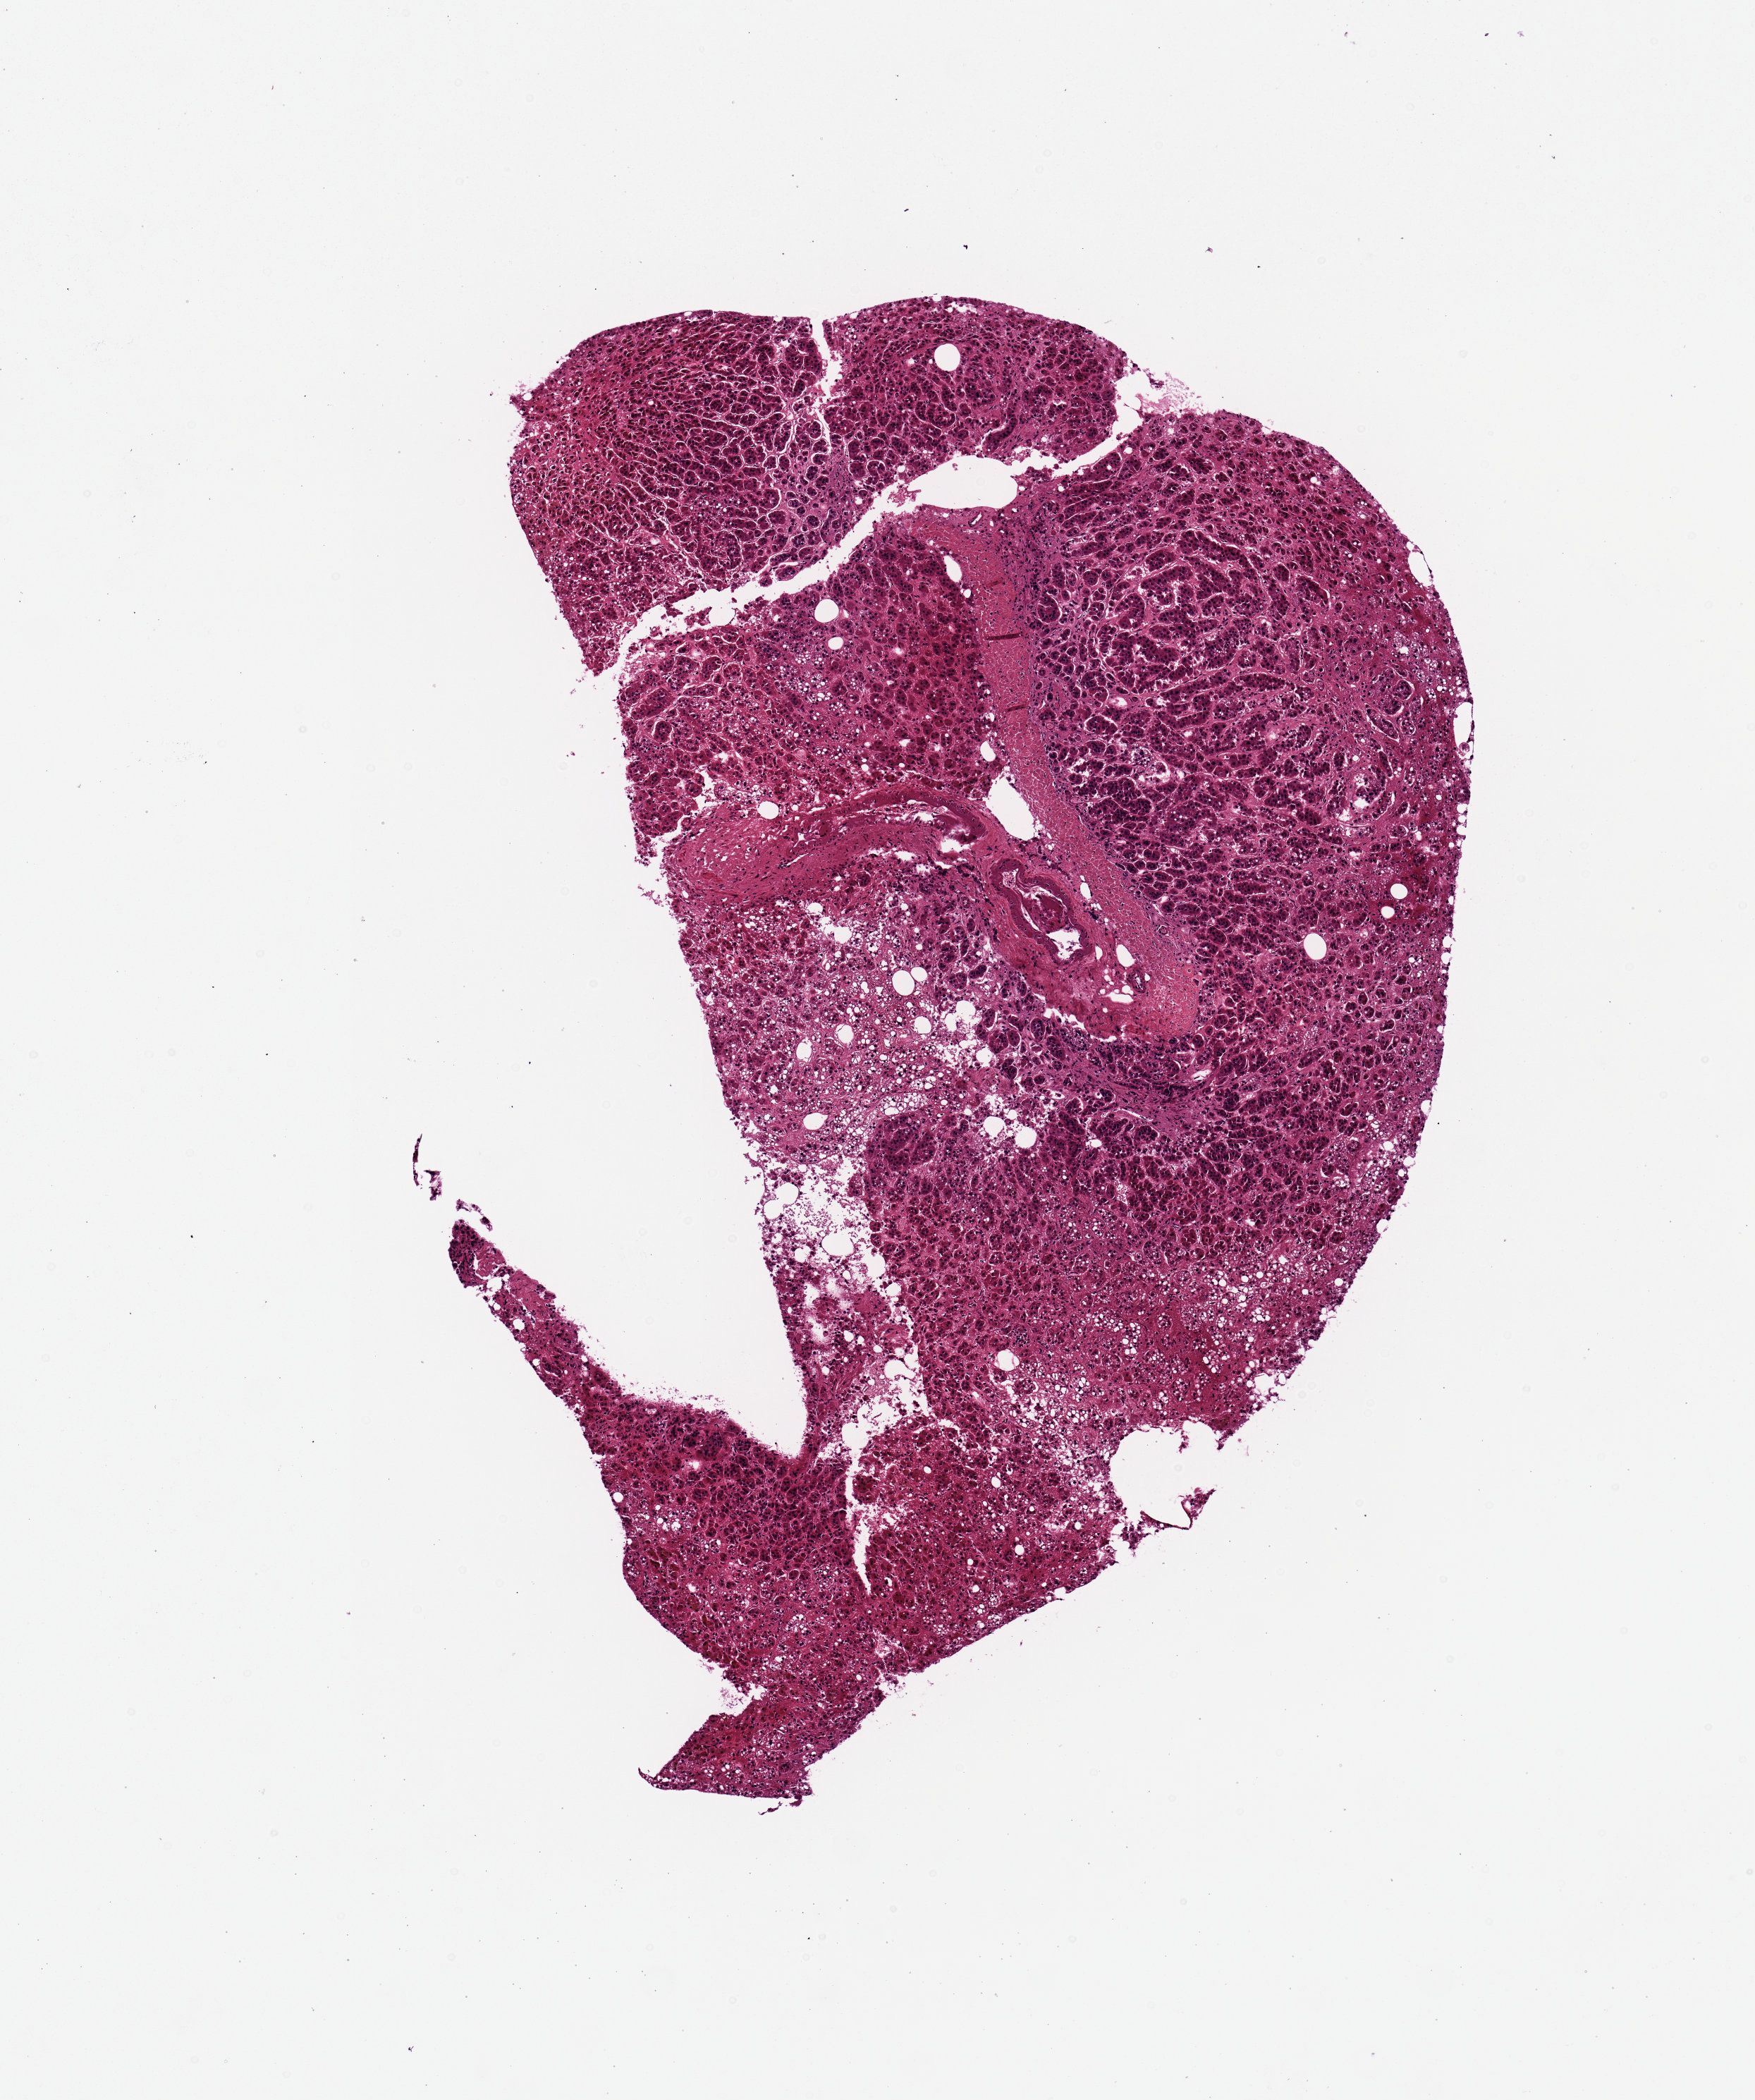
H&E whole-slide image, whole scanned area (about 4.9 x 5.9 mm) shown as a low-resolution overview; PAXgene-fixed paraffin-embedded (PFPE) section; target tissue: adrenal gland; donor tissue sample. Male donor.
Pathologist's review note for this sample: 1 piece; cortex3 pieces.